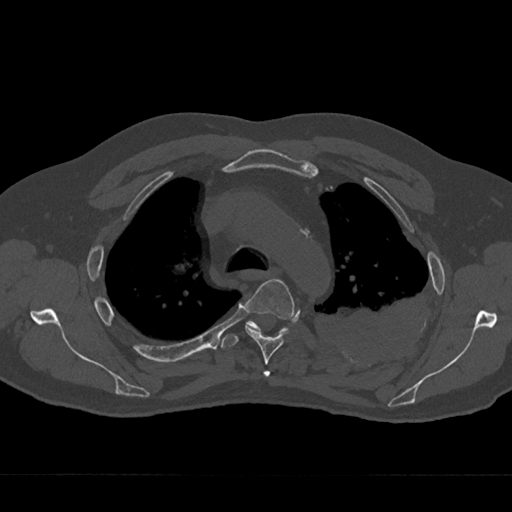
CT including the spine, one axial slice. Position 510 of 797 along the scan axis. Reconstruction kernel Br40s/3. Bone window (W 1800 / L 400 HU). 0.5 mm slice thickness. 512 × 512 image matrix, field of view 377 × 377 mm. Patient: male, 75 years. Case-level facts recorded for this patient, not image findings: primary cancer: renal.
Annotated regions visible in this slice (semi-automatically segmented with operator editing):
- T3 vertebra: bounding box <263,371,270,377> (left, top, right, bottom; pixels)
- T4 vertebra: <245,279,295,376>
- T5 vertebra: <221,320,287,349>